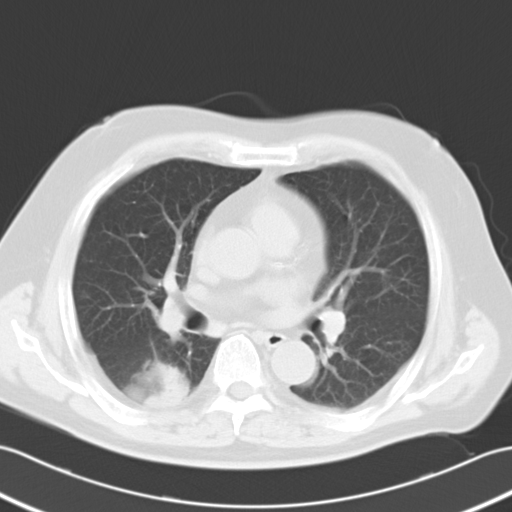
Chest CT, one axial slice; slice 12 of 25 in the series (ordered by position); reconstruction kernel B40f; 120 kVp; lung window (W 1500 / L -600 HU); 10 mm slice thickness; 512 × 512 image matrix, field of view 353 × 353 mm. Patient: male, 70 years. Case-level facts recorded for this patient, not image findings: clinical TNM (as recorded): T2 N0 M0.
Outlined on this slice (rectangle marked by the reading radiologist):
- lung tumour (recorded histology: adenocarcinoma): bounding box [x1, y1, x2, y2] px = [142, 360, 190, 424]